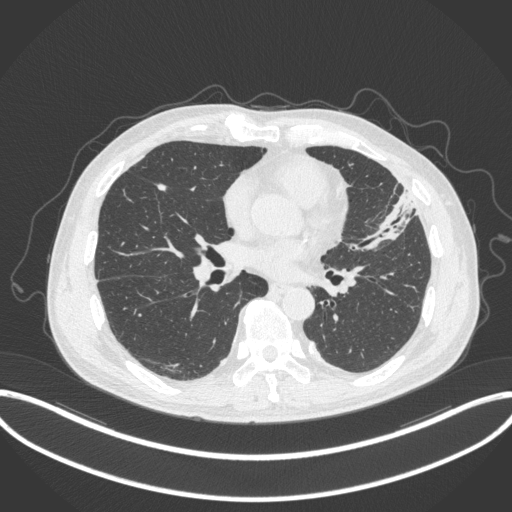
Chest CT, one axial slice. Position 155 of 382 along the scan axis. Reconstruction kernel B31f. Lung window (W 1500 / L -600 HU). 1 mm slice thickness. 512 × 512 image matrix. Male patient, age 64 years. Case-level facts recorded for this patient, not image findings: clinical TNM (as recorded): T4 N1 M0; histopathological grade: G3.
Annotated regions visible in this slice (rectangle marked by the reading radiologist):
- lung tumour (recorded histology: adenocarcinoma): bounding box (x1, y1, x2, y2) in pixels: (365, 185, 415, 251)